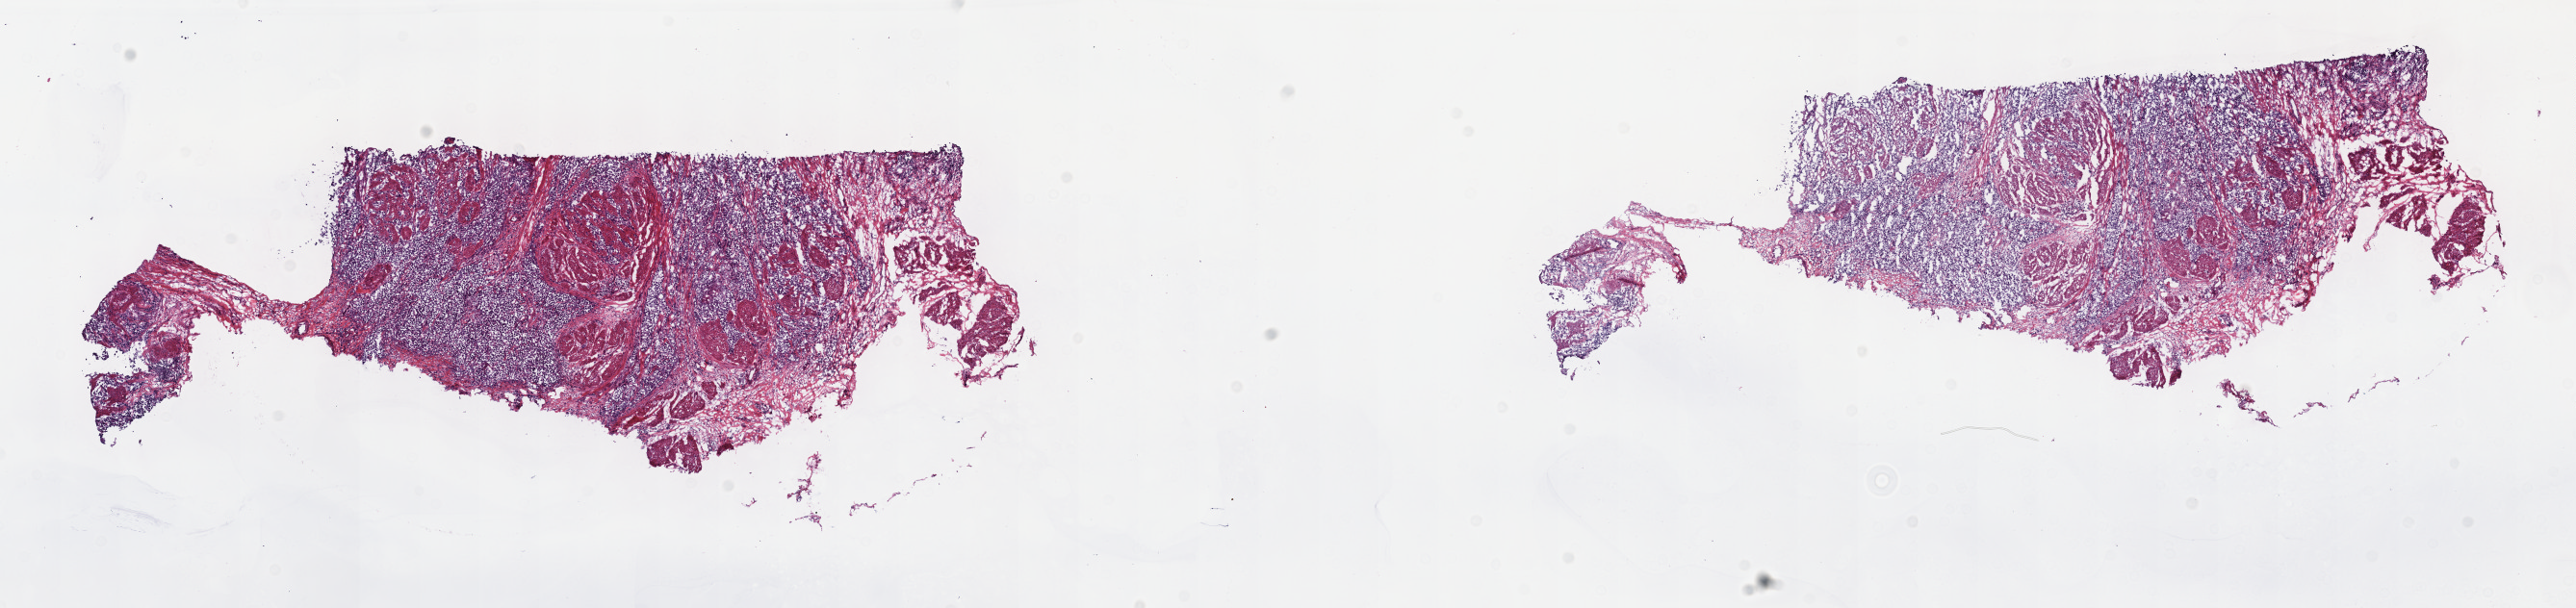
Digitized H&E-stained tissue section (whole slide), shown as a low-resolution overview of the whole scanned area (about 21.6 x 5.1 mm, slide scanned at 40x), frozen section from the top of the tissue portion, primary tumour sample from the bladder. Patient: female, age at initial diagnosis 67 years. Histologic grade: high grade. Slide review estimates, as recorded: tumour cells 100%, tumour nuclei 75%, normal cells 0%, stromal cells 0%, necrosis 0%. Inflammatory infiltration, as recorded: lymphocyte infiltration 2%, monocyte infiltration 0%, neutrophil infiltration 0%.
Histologic diagnosis: Transitional cell carcinoma. AJCC pathologic stage: II (6th edition).